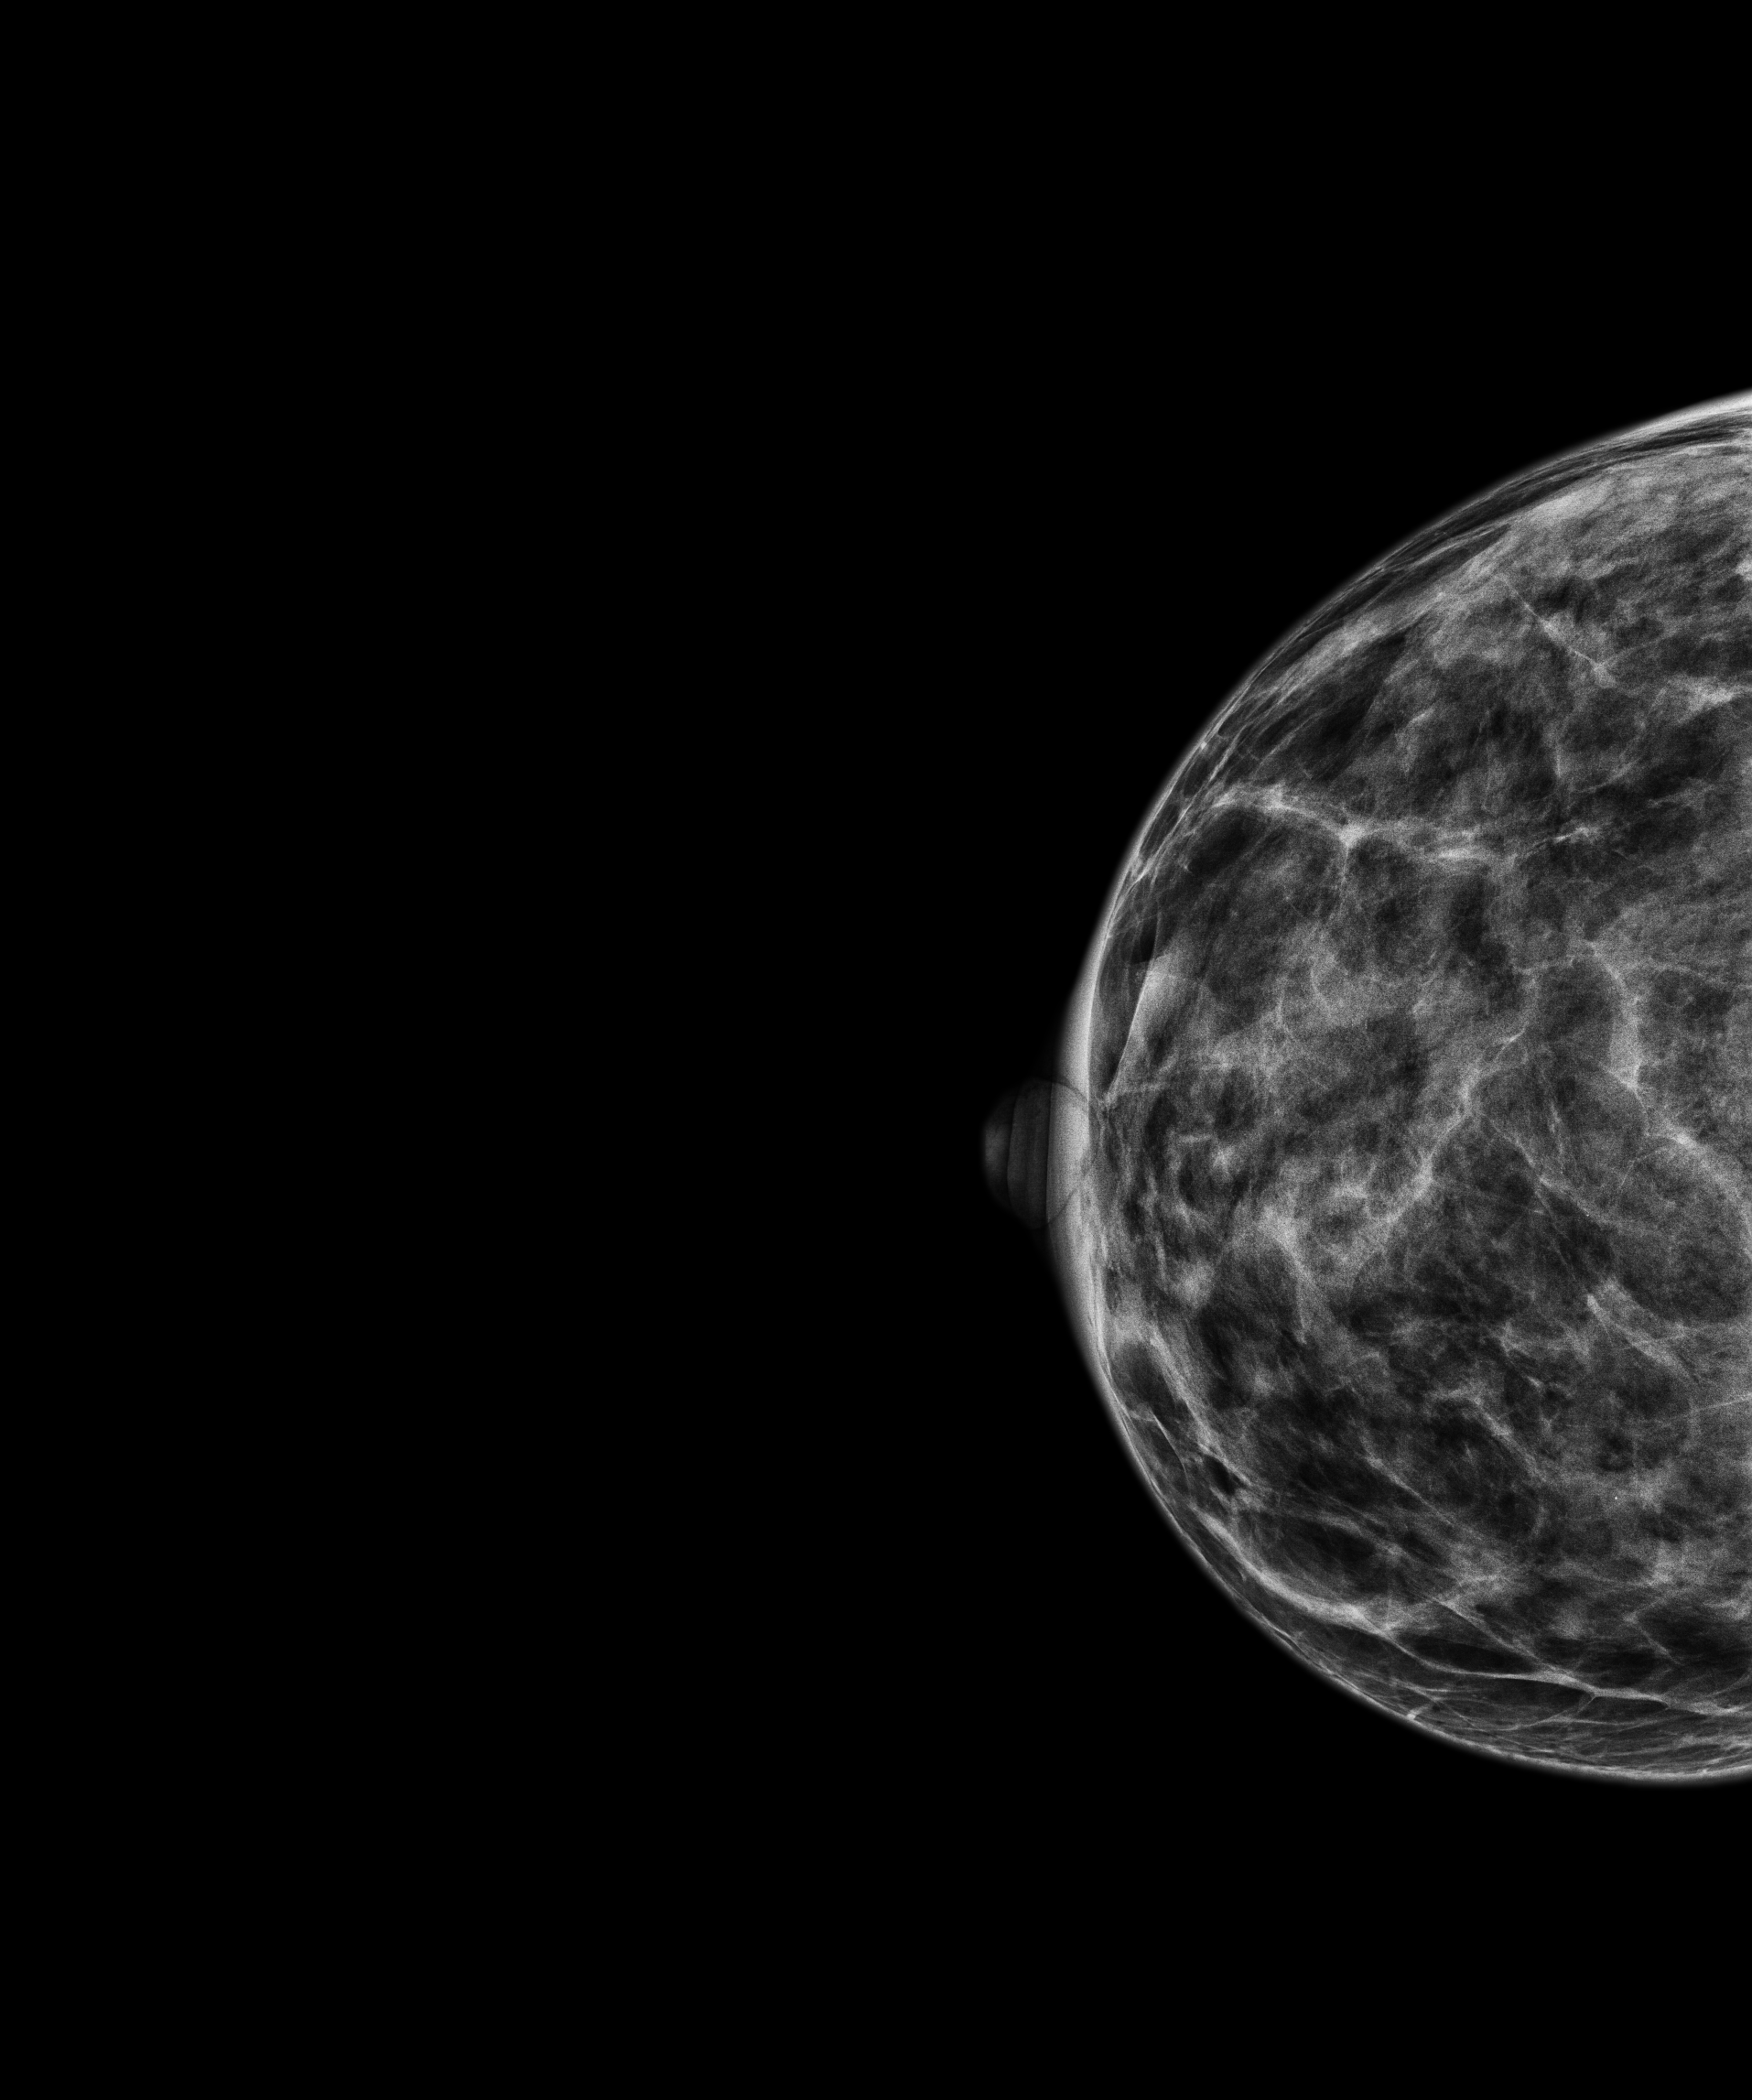
Annual screening mammography examination; compressed breast thickness 27.6 mm. Patient: female, 46 years.
Image type: full-field digital mammogram. Breast: right. Projection: craniocaudal (CC) view.